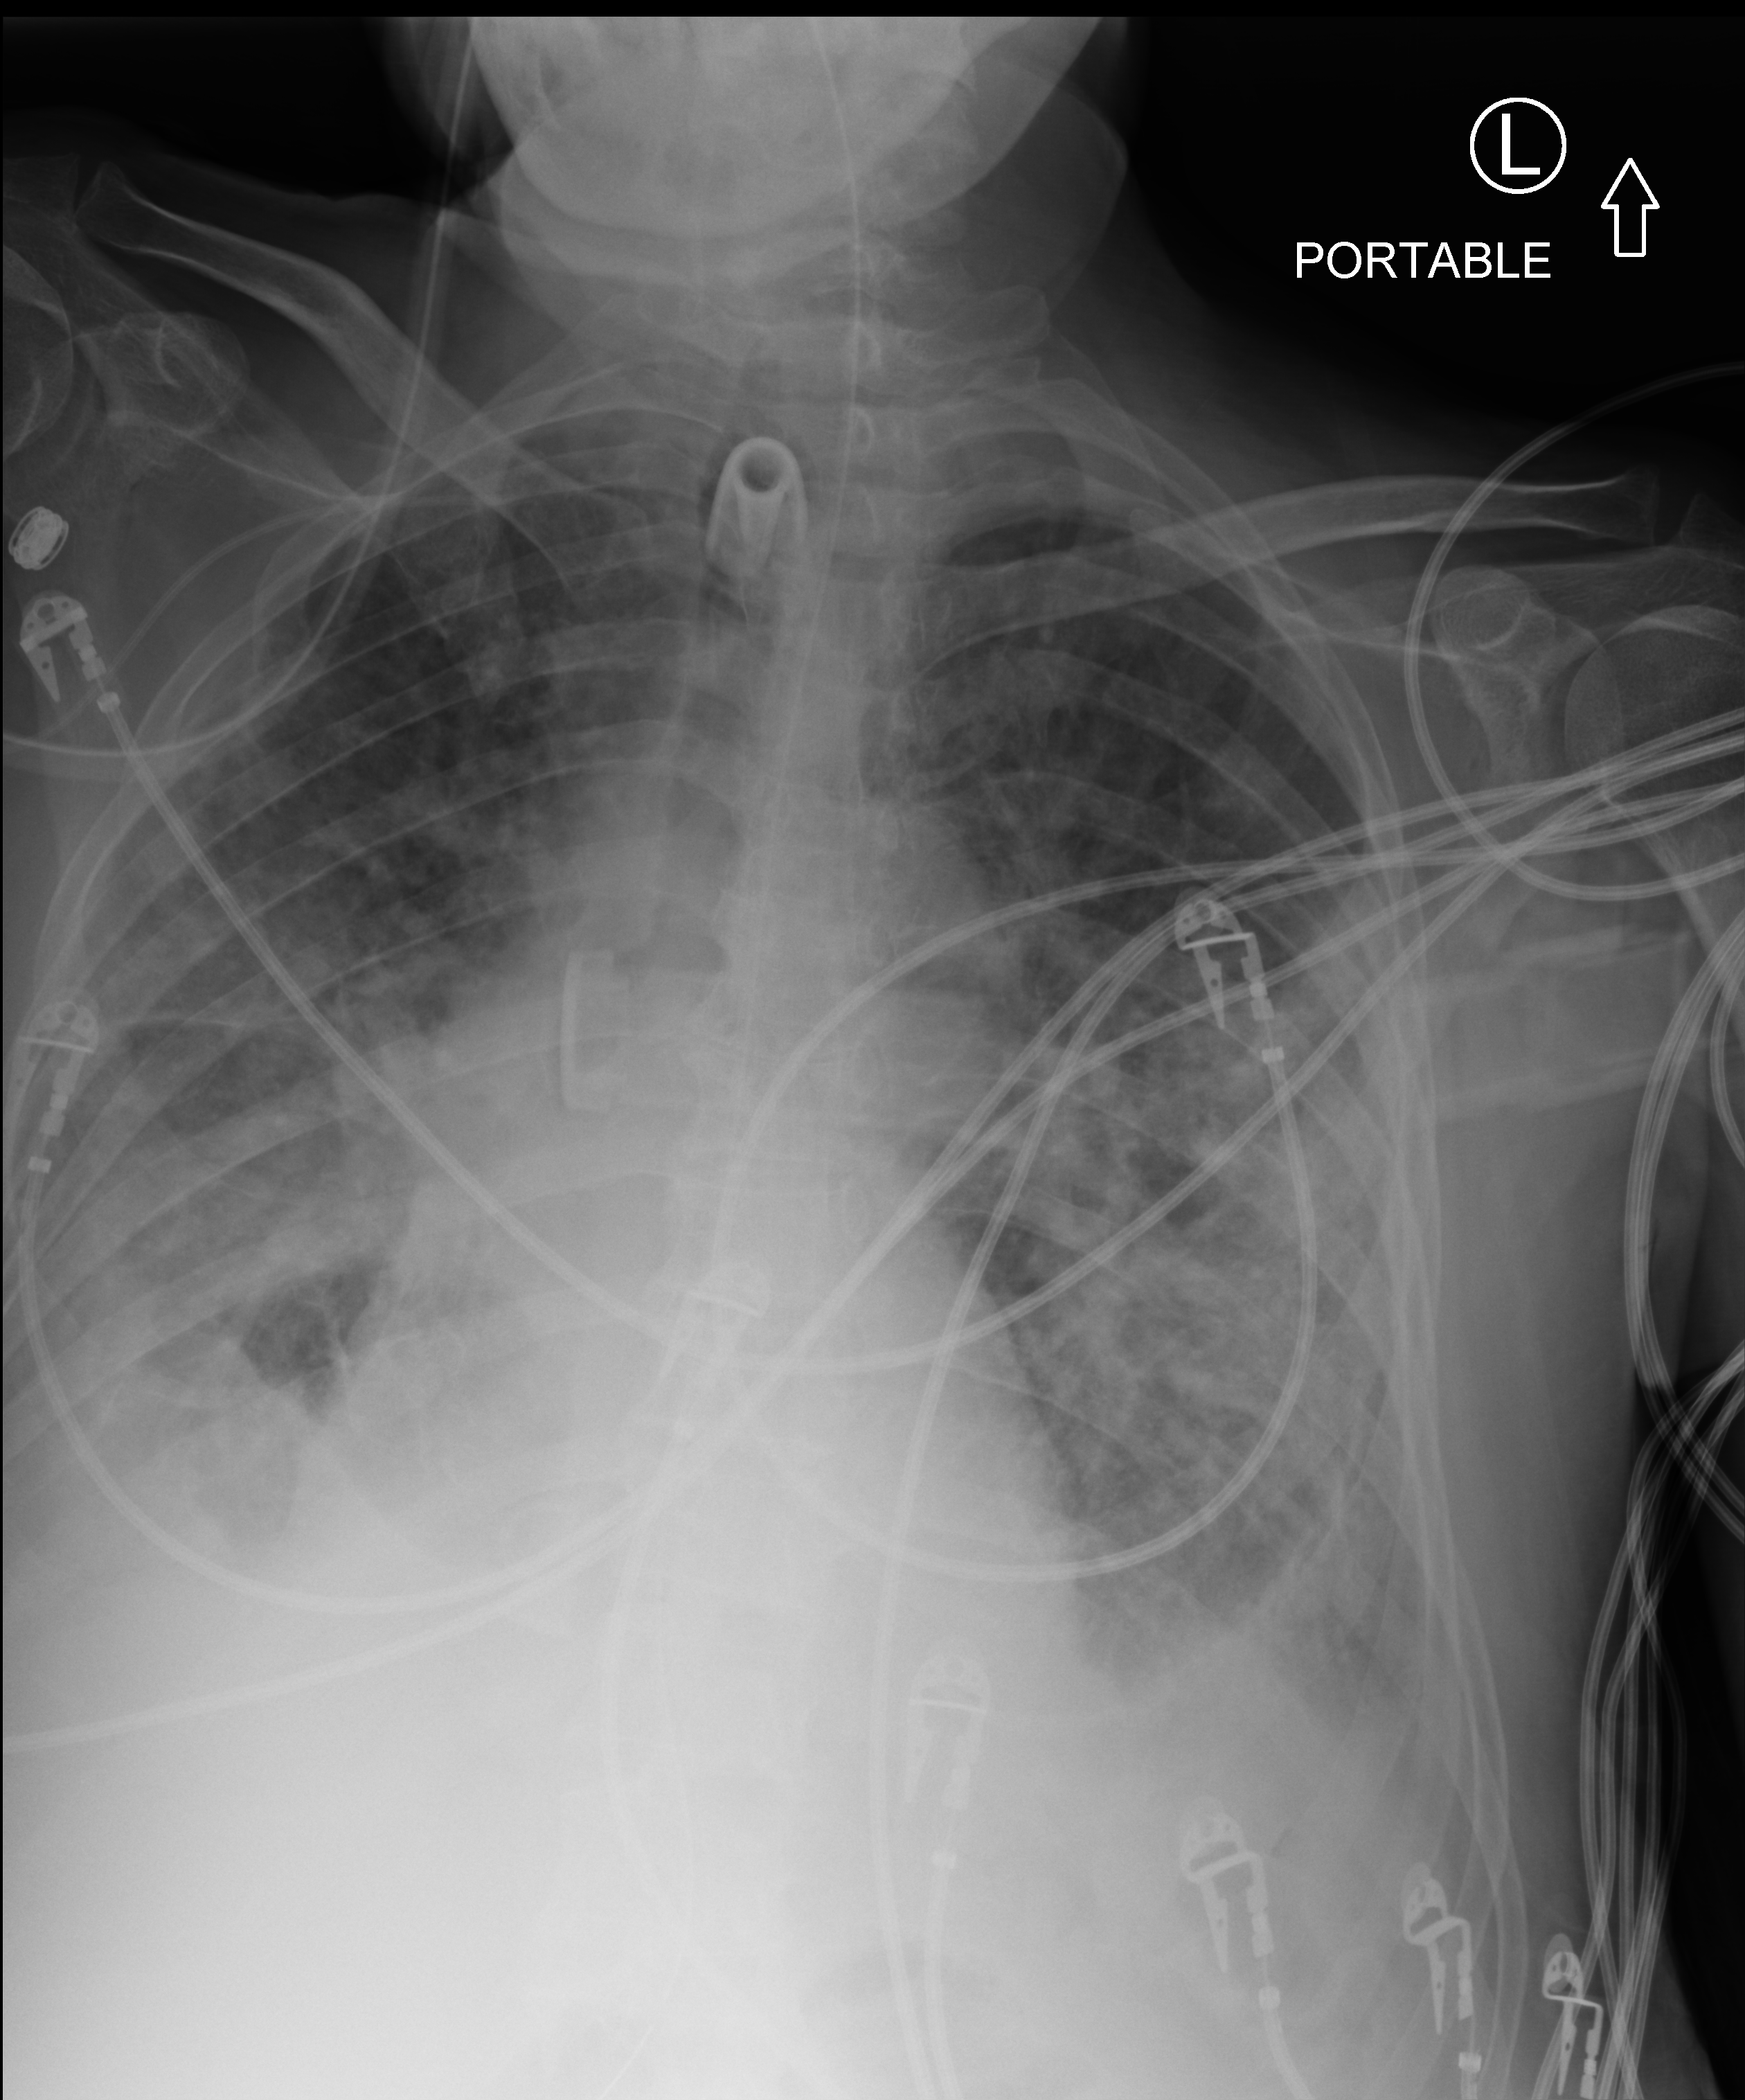
Portable chest radiograph, anteroposterior (AP) projection. Male patient hospitalised with COVID-19, age 75–90 years.
Hospital-stay facts (about this admission, not read from this image; timing relative to this image not recorded):
- diabetes (admission record): no
- admitted to intensive care during this hospital stay: yes
- mechanically ventilated during this hospital stay: yes